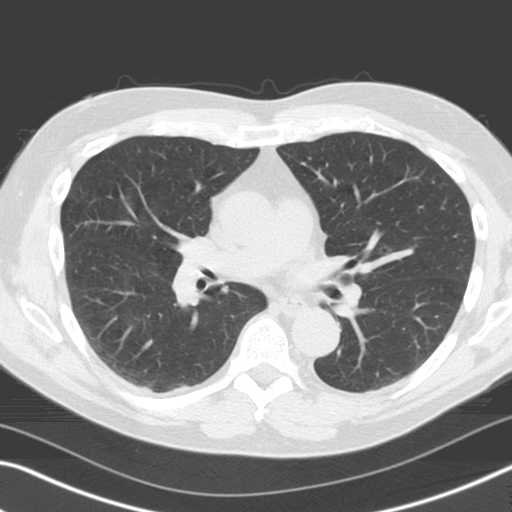
Low-dose screening chest CT, axial slice, baseline screening round, lung window (W 1500 / L -600 HU), 3.2 mm slice thickness, standard (soft-tissue) reconstruction kernel (C), slice 82 of 165 in the series. Male, age 71 years at enrolment. Former smoker at enrolment.
- Expert-annotated lung lesion, bounding box (x1, y1, x2, y2) in pixels: (397, 155, 442, 194).
- Reader record for this screening exam (exam-level; its link to the box is not recorded): non-calcified nodule or mass ≥4 mm, left upper lobe, 11 × 10 mm, poorly defined margins, ground glass attenuation.
- Official screen result: positive, change unspecified: nodule(s) >= 4 mm or enlarging nodule(s), mass(es), or other non-specific abnormalities suspicious for lung cancer.
- Participant outcome: lung cancer diagnosed 289 days after this screen — adenocarcinoma, NOS, left upper lobe, moderately differentiated (G2), stage IA (AJCC 6th edition), 11 mm at pathology.